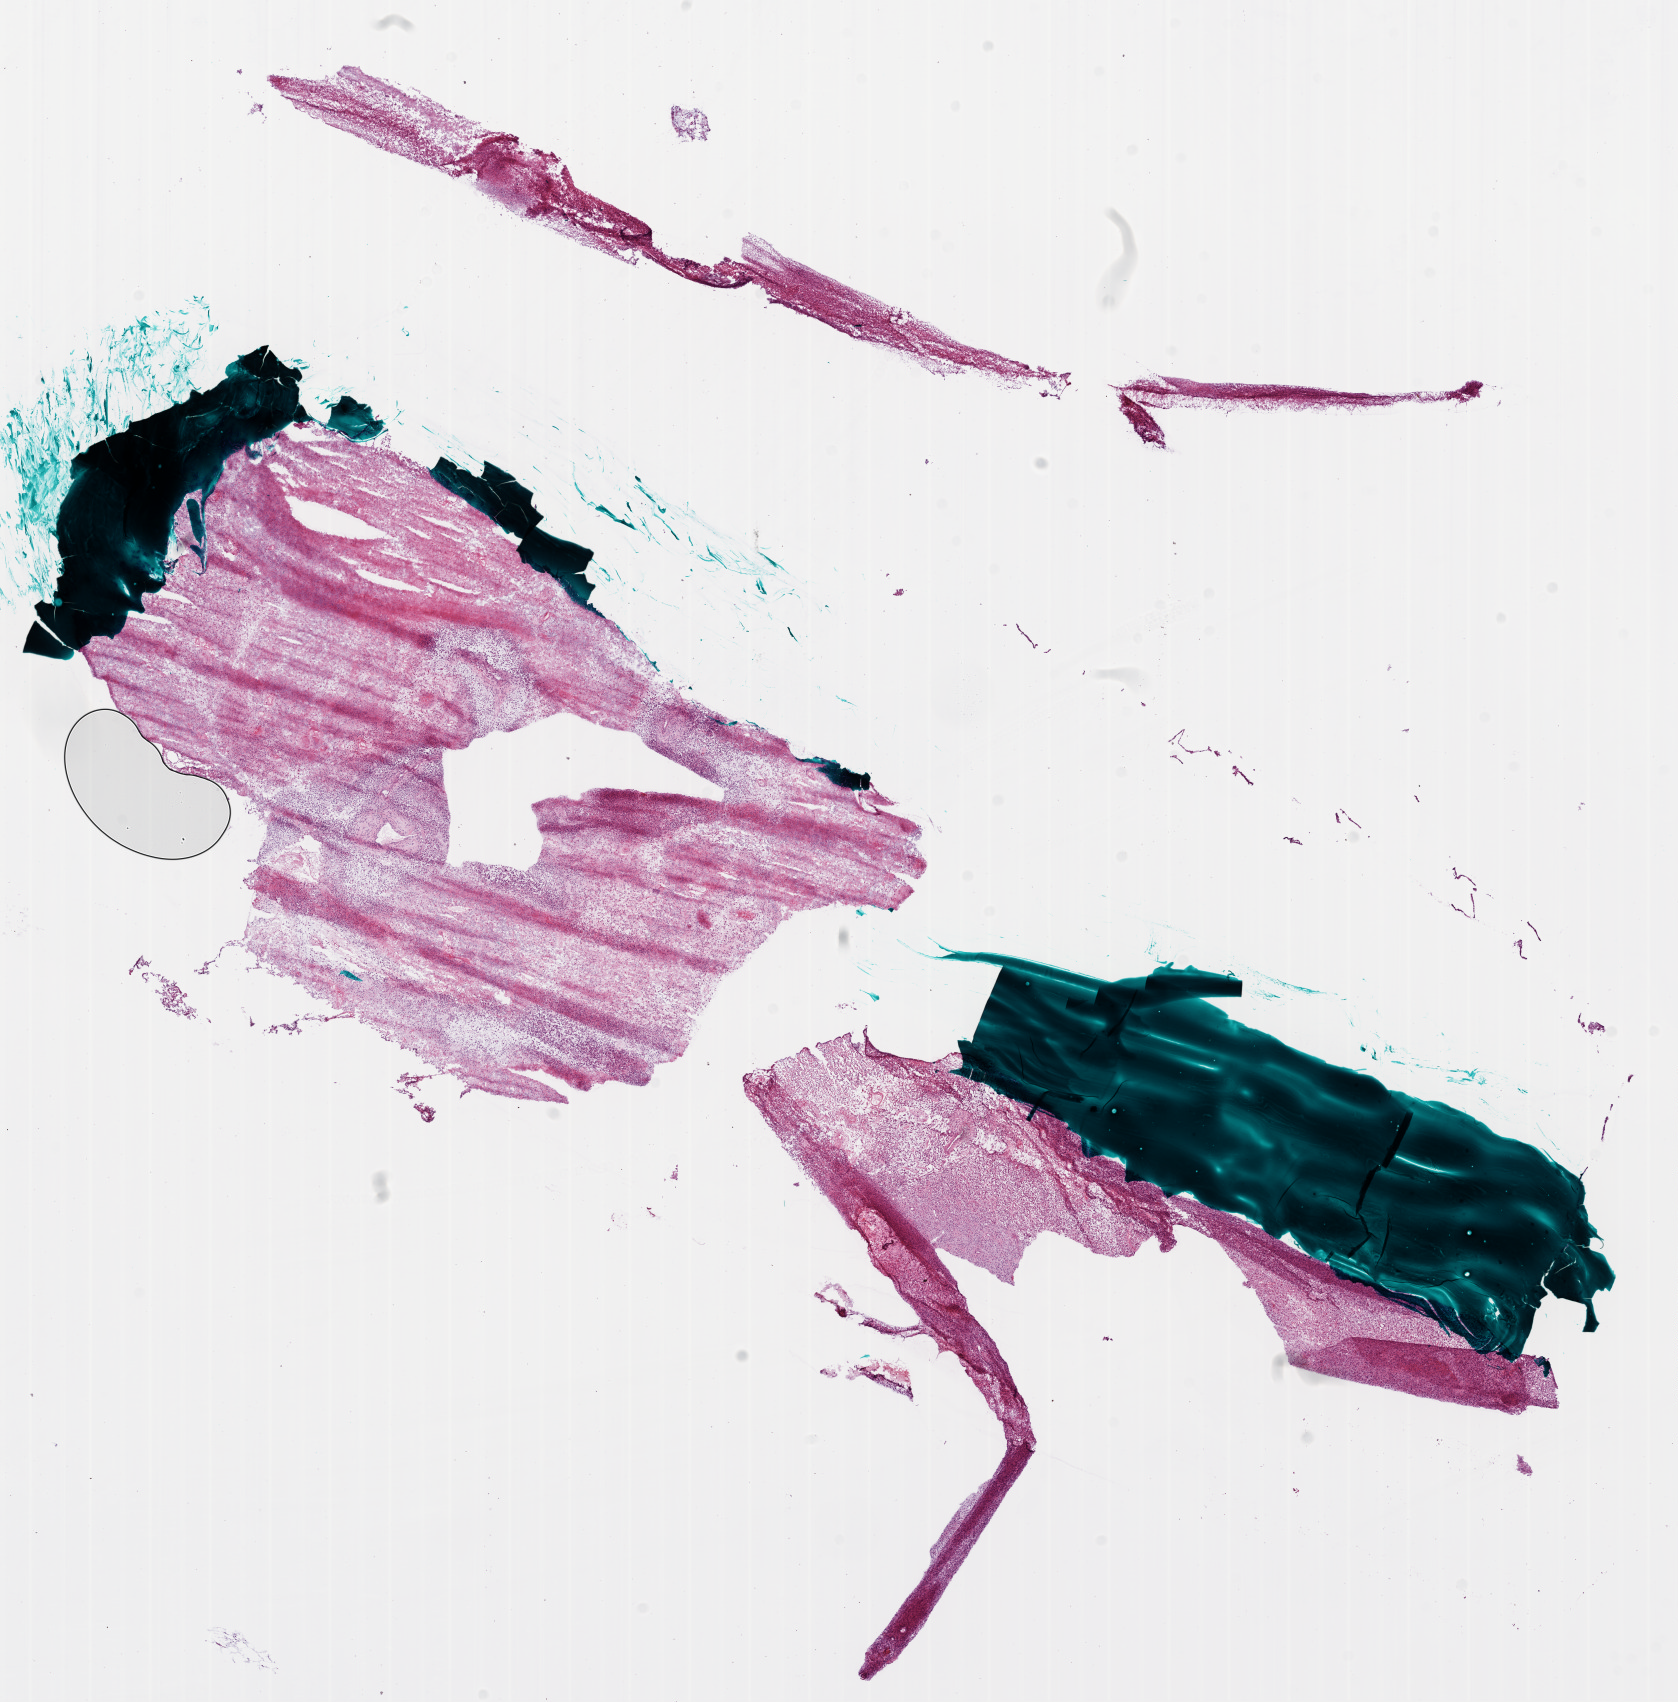
Hematoxylin and eosin (H&E) stained whole-slide image, low-resolution overview of the scanned area, about 13.5 x 13.7 mm (slide scanned at 20x); frozen section; brain, primary tumour sample. Patient: male, age at initial diagnosis 54 years. Slide review estimates, as recorded: tumour cells 55%, tumour nuclei 90%, normal cells 5%, stromal cells 0%, necrosis 40%.
Diagnosis: Glioblastoma.